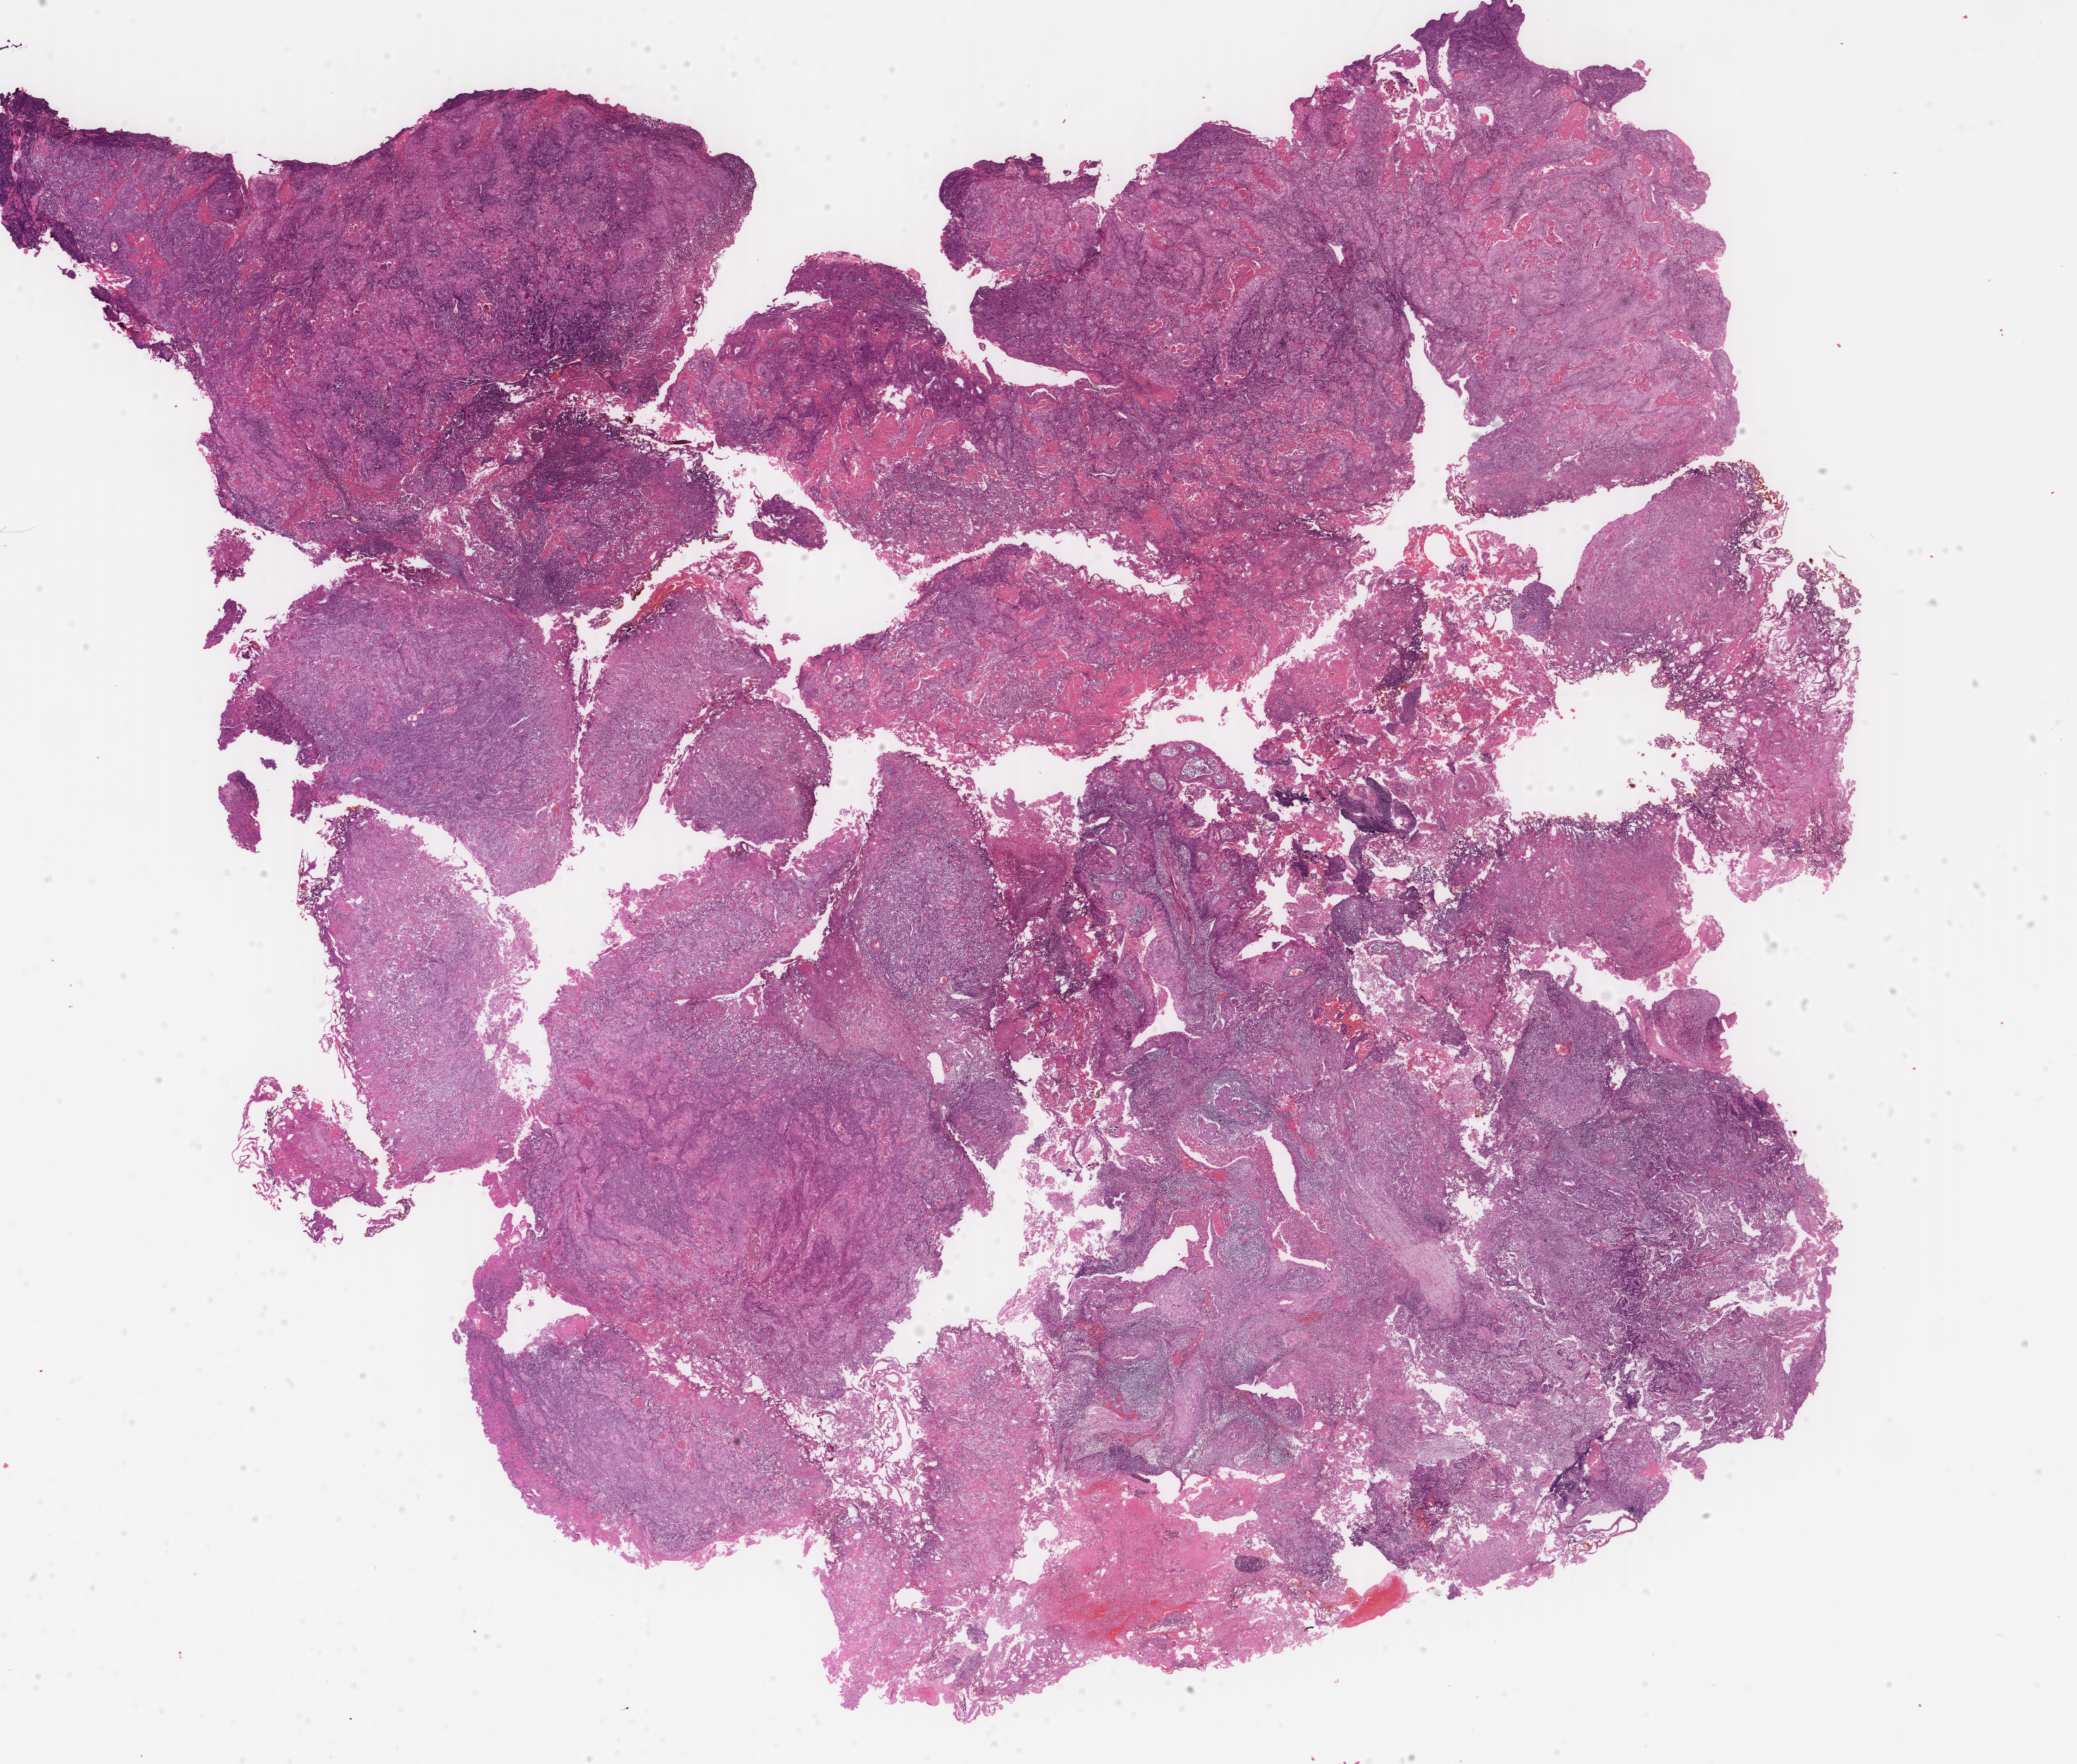
Digitized H&E tissue section (whole slide) — whole scanned area (about 23.4 x 19.8 mm, slide scanned at 40x) shown as a low-resolution overview. Formalin-fixed paraffin-embedded (FFPE) diagnostic section. Sample: primary tumour, bladder. Patient: female, age at initial diagnosis 56 years. Histologic grade: high grade.
- histologic diagnosis: Transitional cell carcinoma
- TNM: N0 M0
- AJCC pathologic stage: II